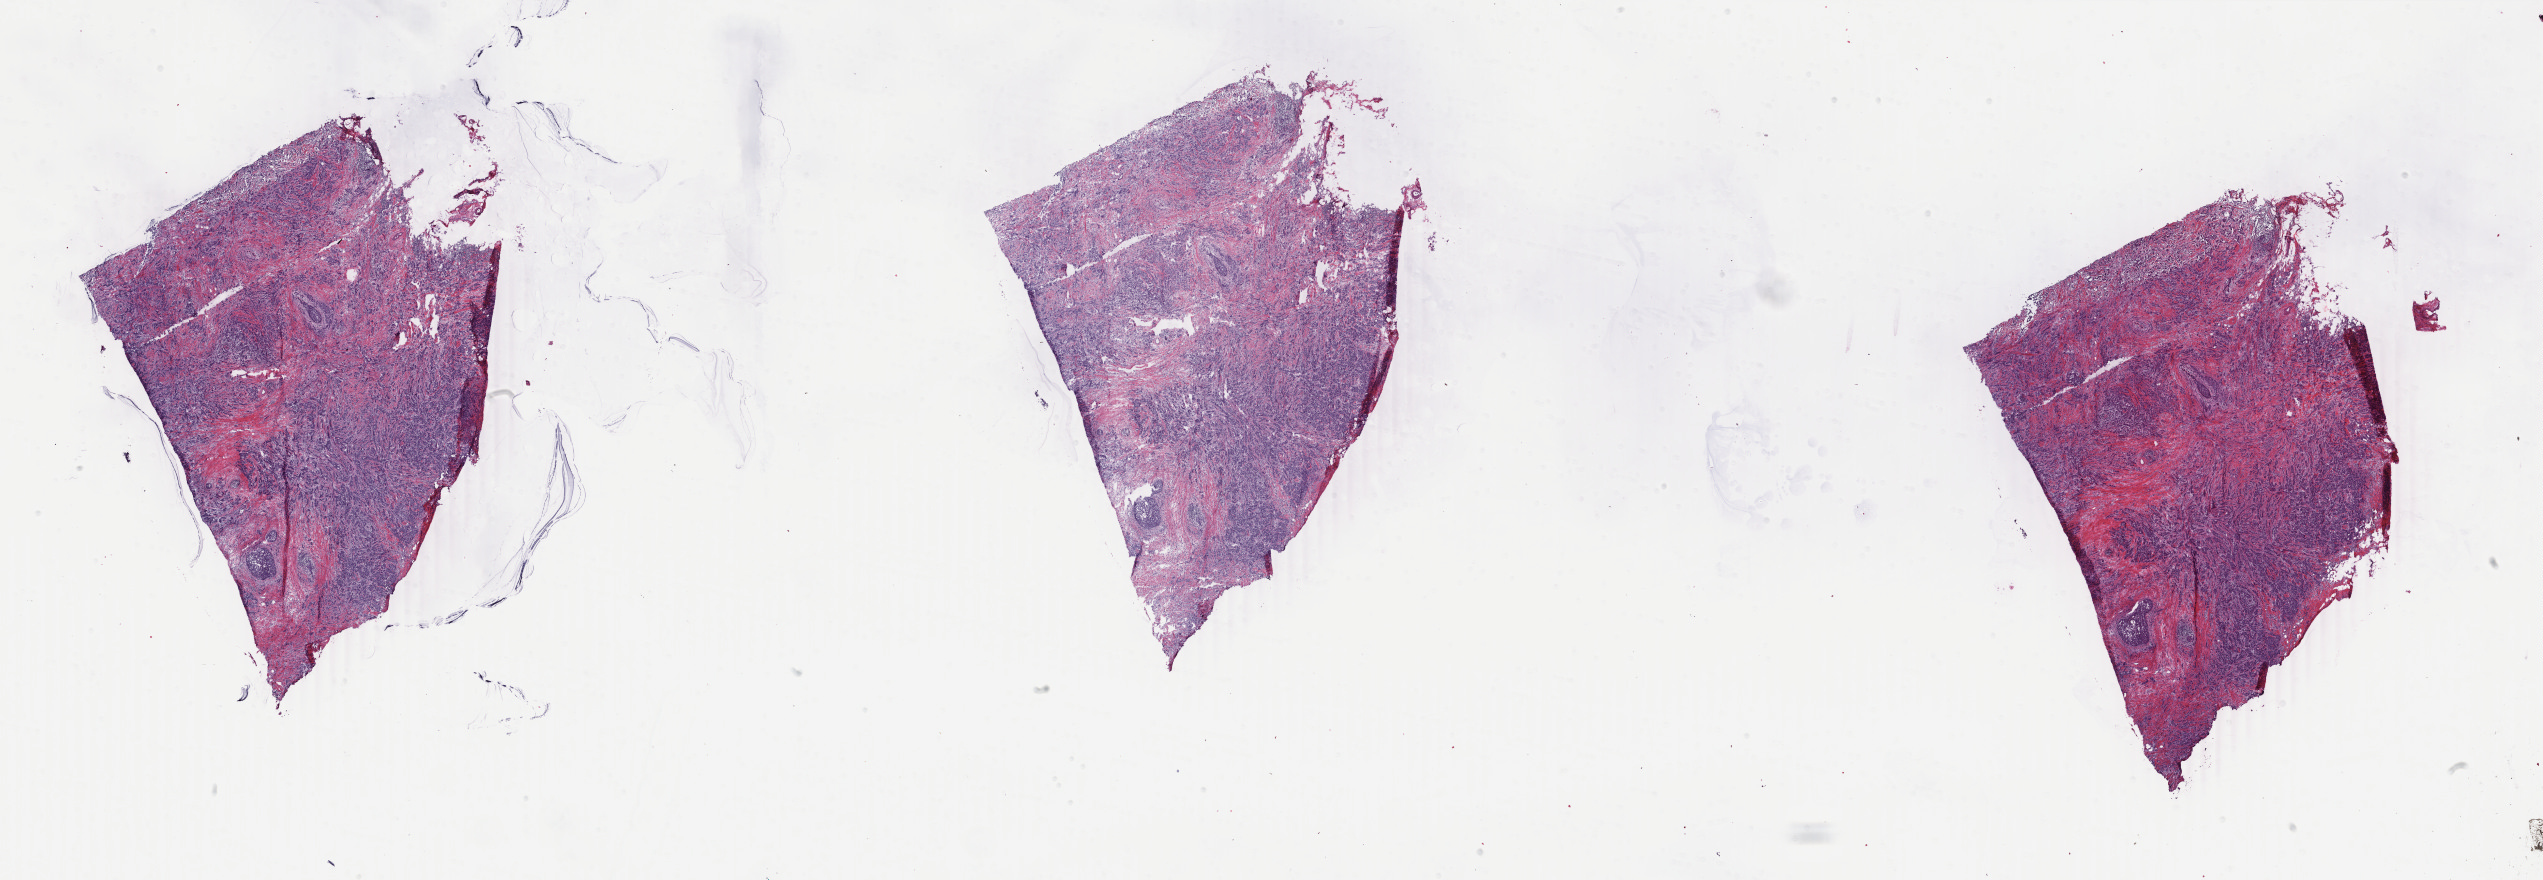
Whole-slide histology image, Hematoxylin and eosin (H&E) stained, shown as a low-resolution overview of the whole scanned area (about 40.5 x 14.0 mm); frozen section; primary tumour sample from the breast. Female patient; age at initial diagnosis 53 years. Slide review estimates, as recorded: tumour cells 85%, tumour nuclei 85%, normal cells 1%, stromal cells 14%, necrosis 0%. Infiltration values recorded for this section: lymphocyte infiltration 1%, monocyte infiltration 0%, neutrophil infiltration 0%.
• histologic diagnosis: Infiltrating duct carcinoma, NOS
• TNM: T2 N2a M0
• AJCC pathologic stage: IIIA